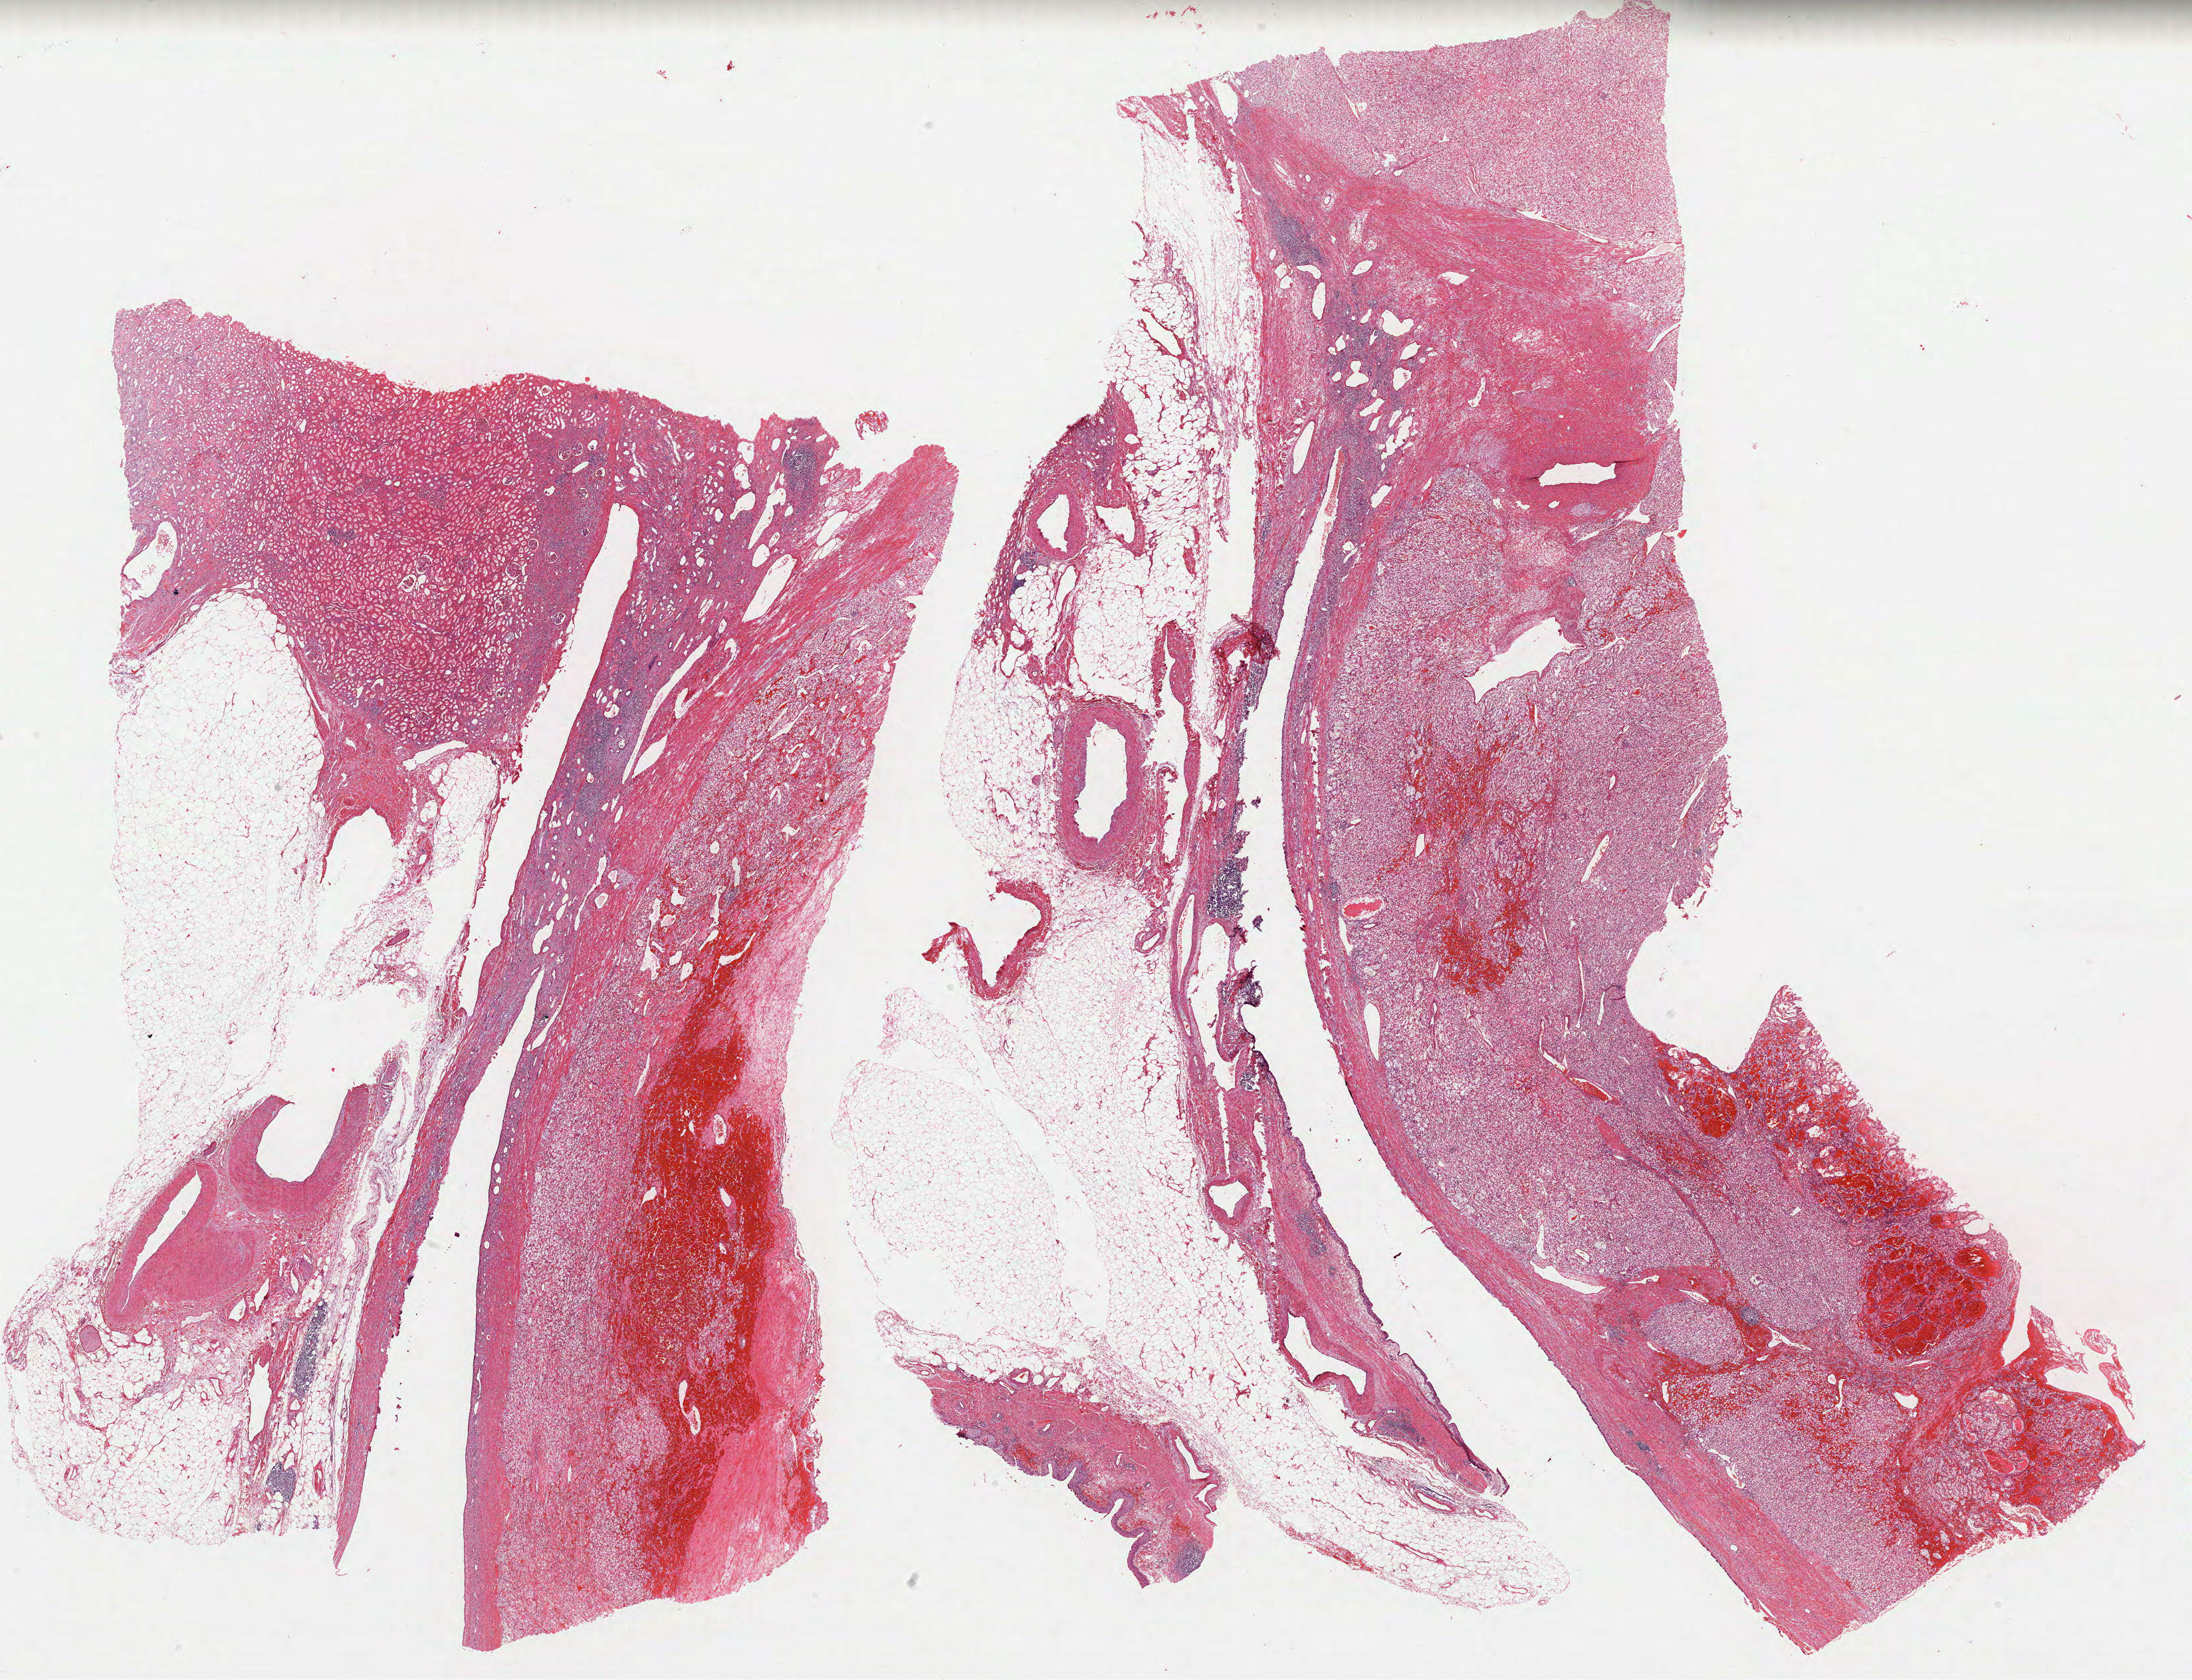
Whole-slide histology image, H&E-stained, low-resolution overview of the scanned area, about 26.6 x 20.4 mm (from a 40x scan); formalin-fixed paraffin-embedded (FFPE) diagnostic section; primary tumour sample from the kidney. Patient: male, age at initial diagnosis 60 years. Histologic grade: G2 (moderately differentiated).
- diagnosis: Clear cell adenocarcinoma, NOS
- AJCC pathologic stage: II (6th edition)
- laterality: right
- lymph nodes positive (case pathology): 0 of 1 examined